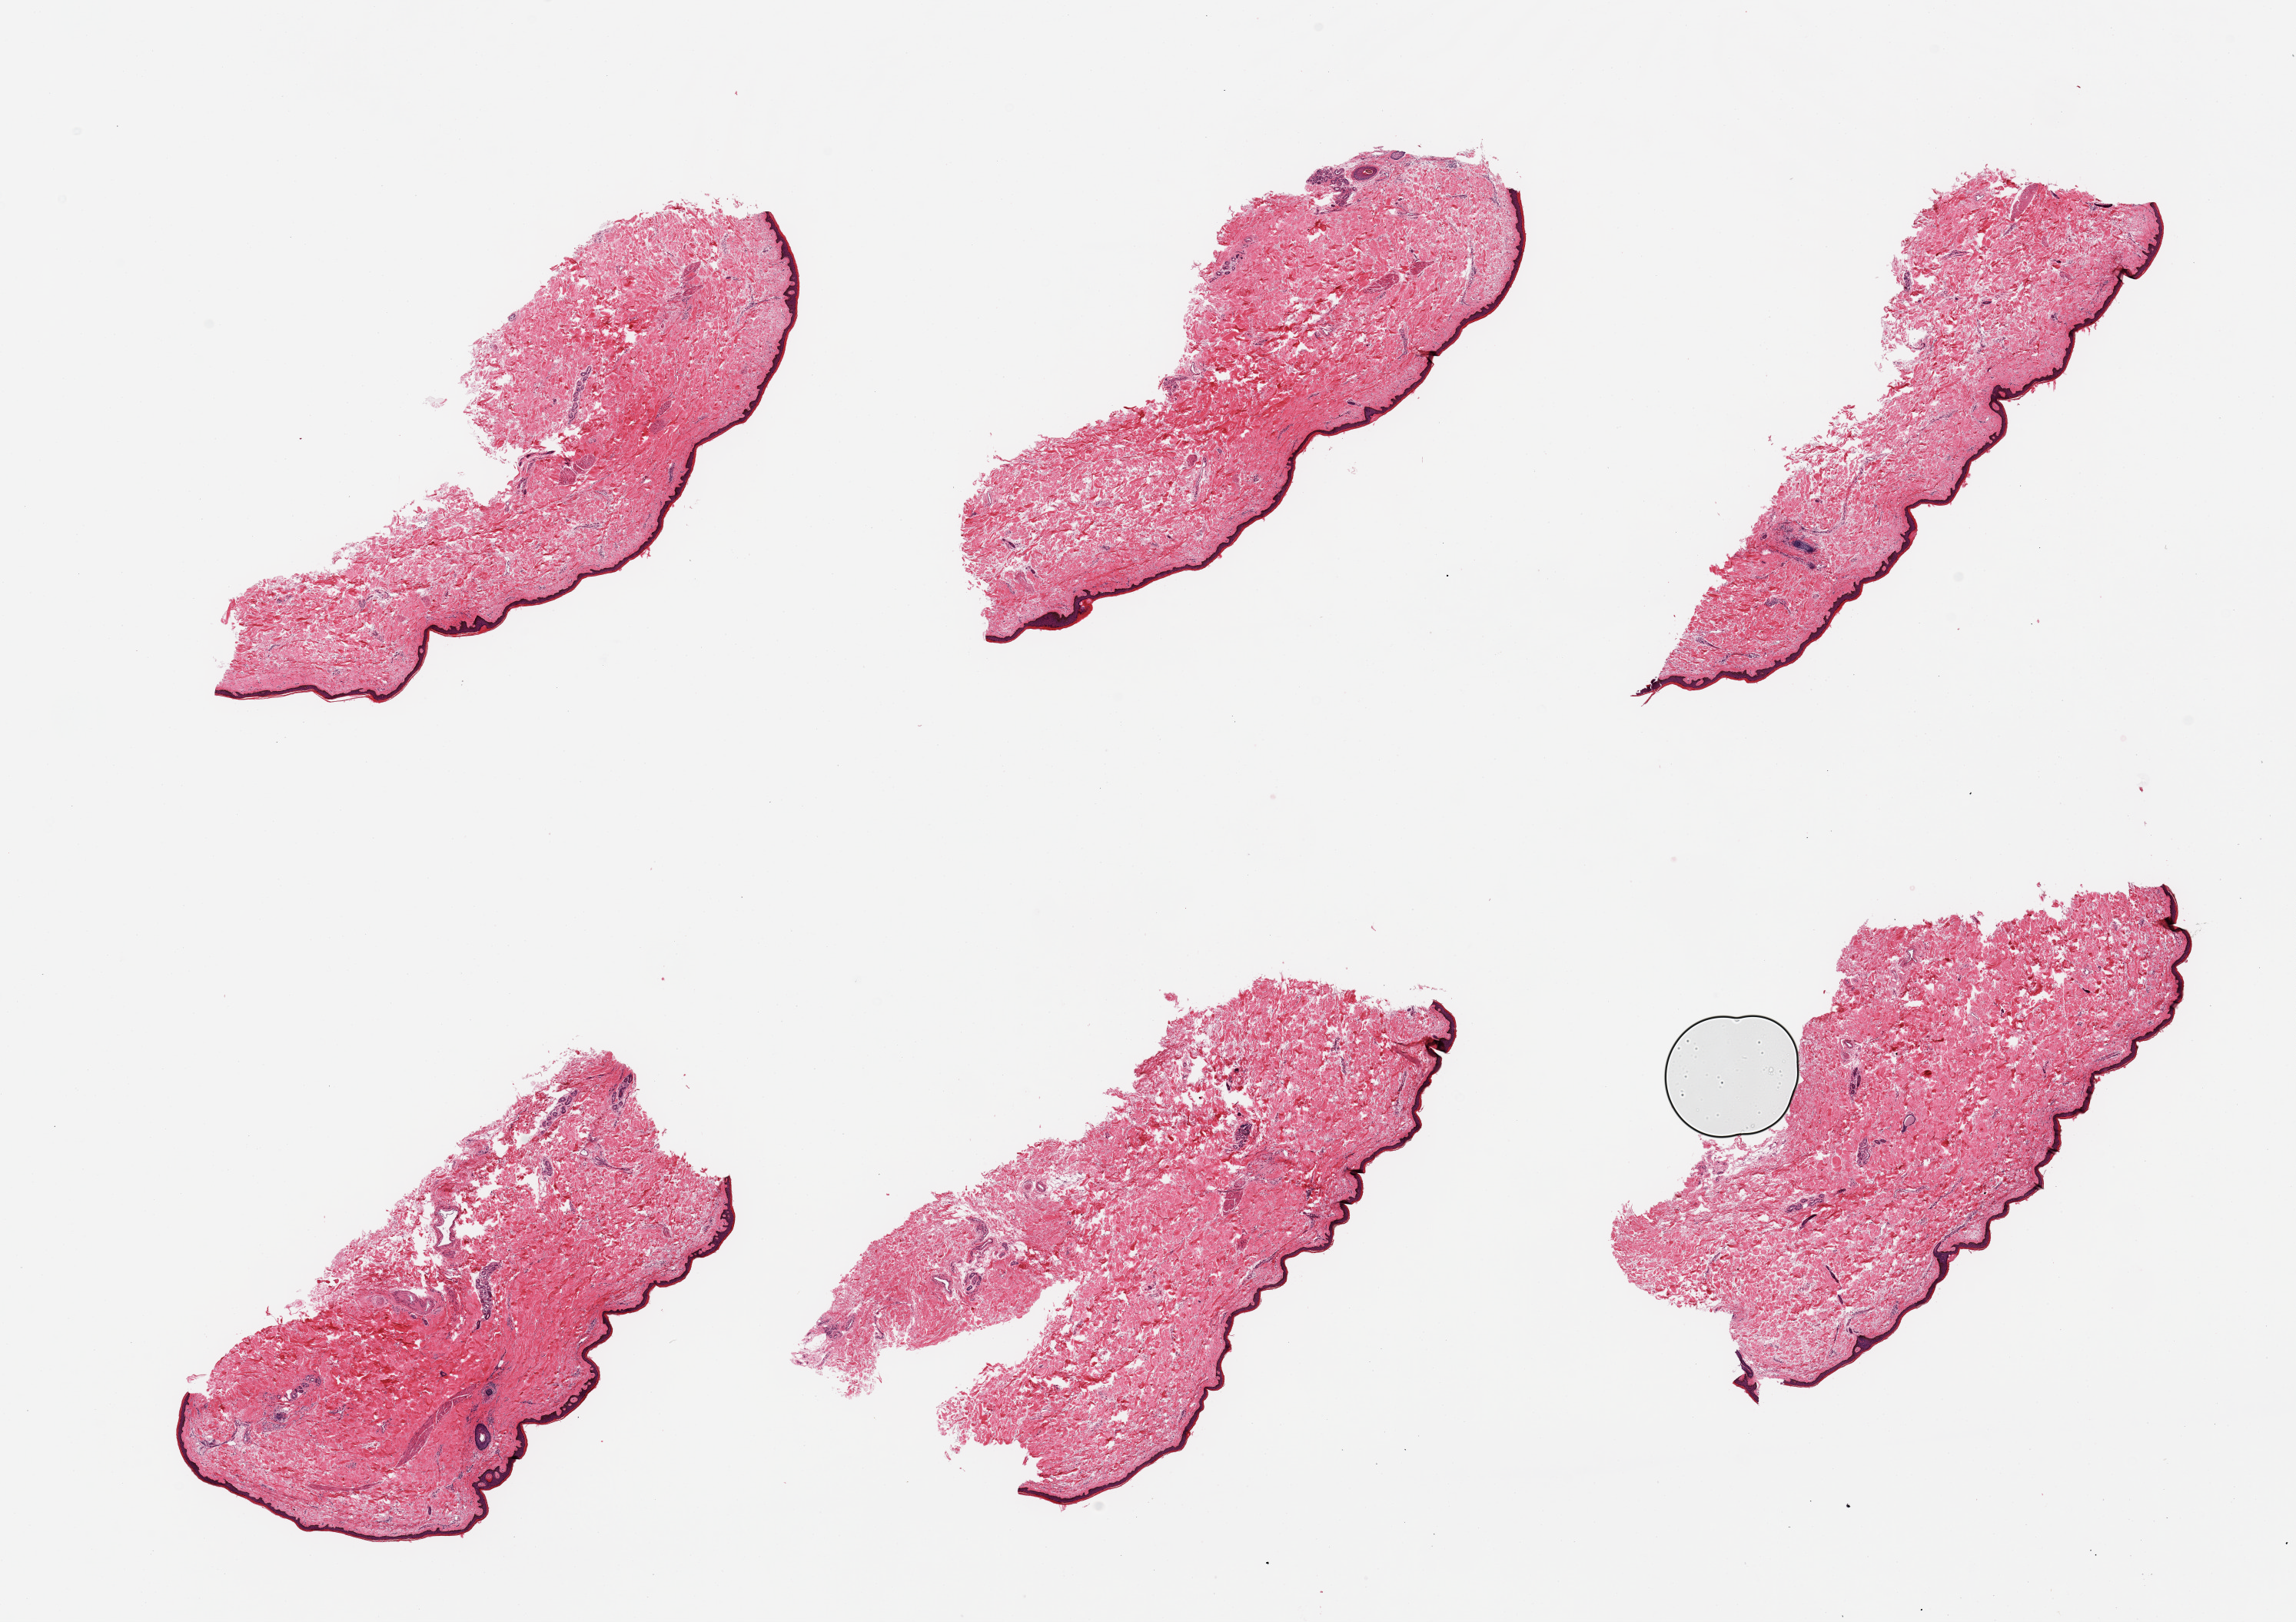
Whole-slide image, hematoxylin and eosin (H&E) stain, a low-resolution overview of the entire scanned area, about 23.6 x 16.7 mm. PAXgene-fixed, paraffin-embedded tissue. Sampled site (target tissue): skin of lower leg. Donor tissue sample. Male donor.
• pathologist's review note for this sample: 6 pieces; well trimmed, epidermis measures 34 microns